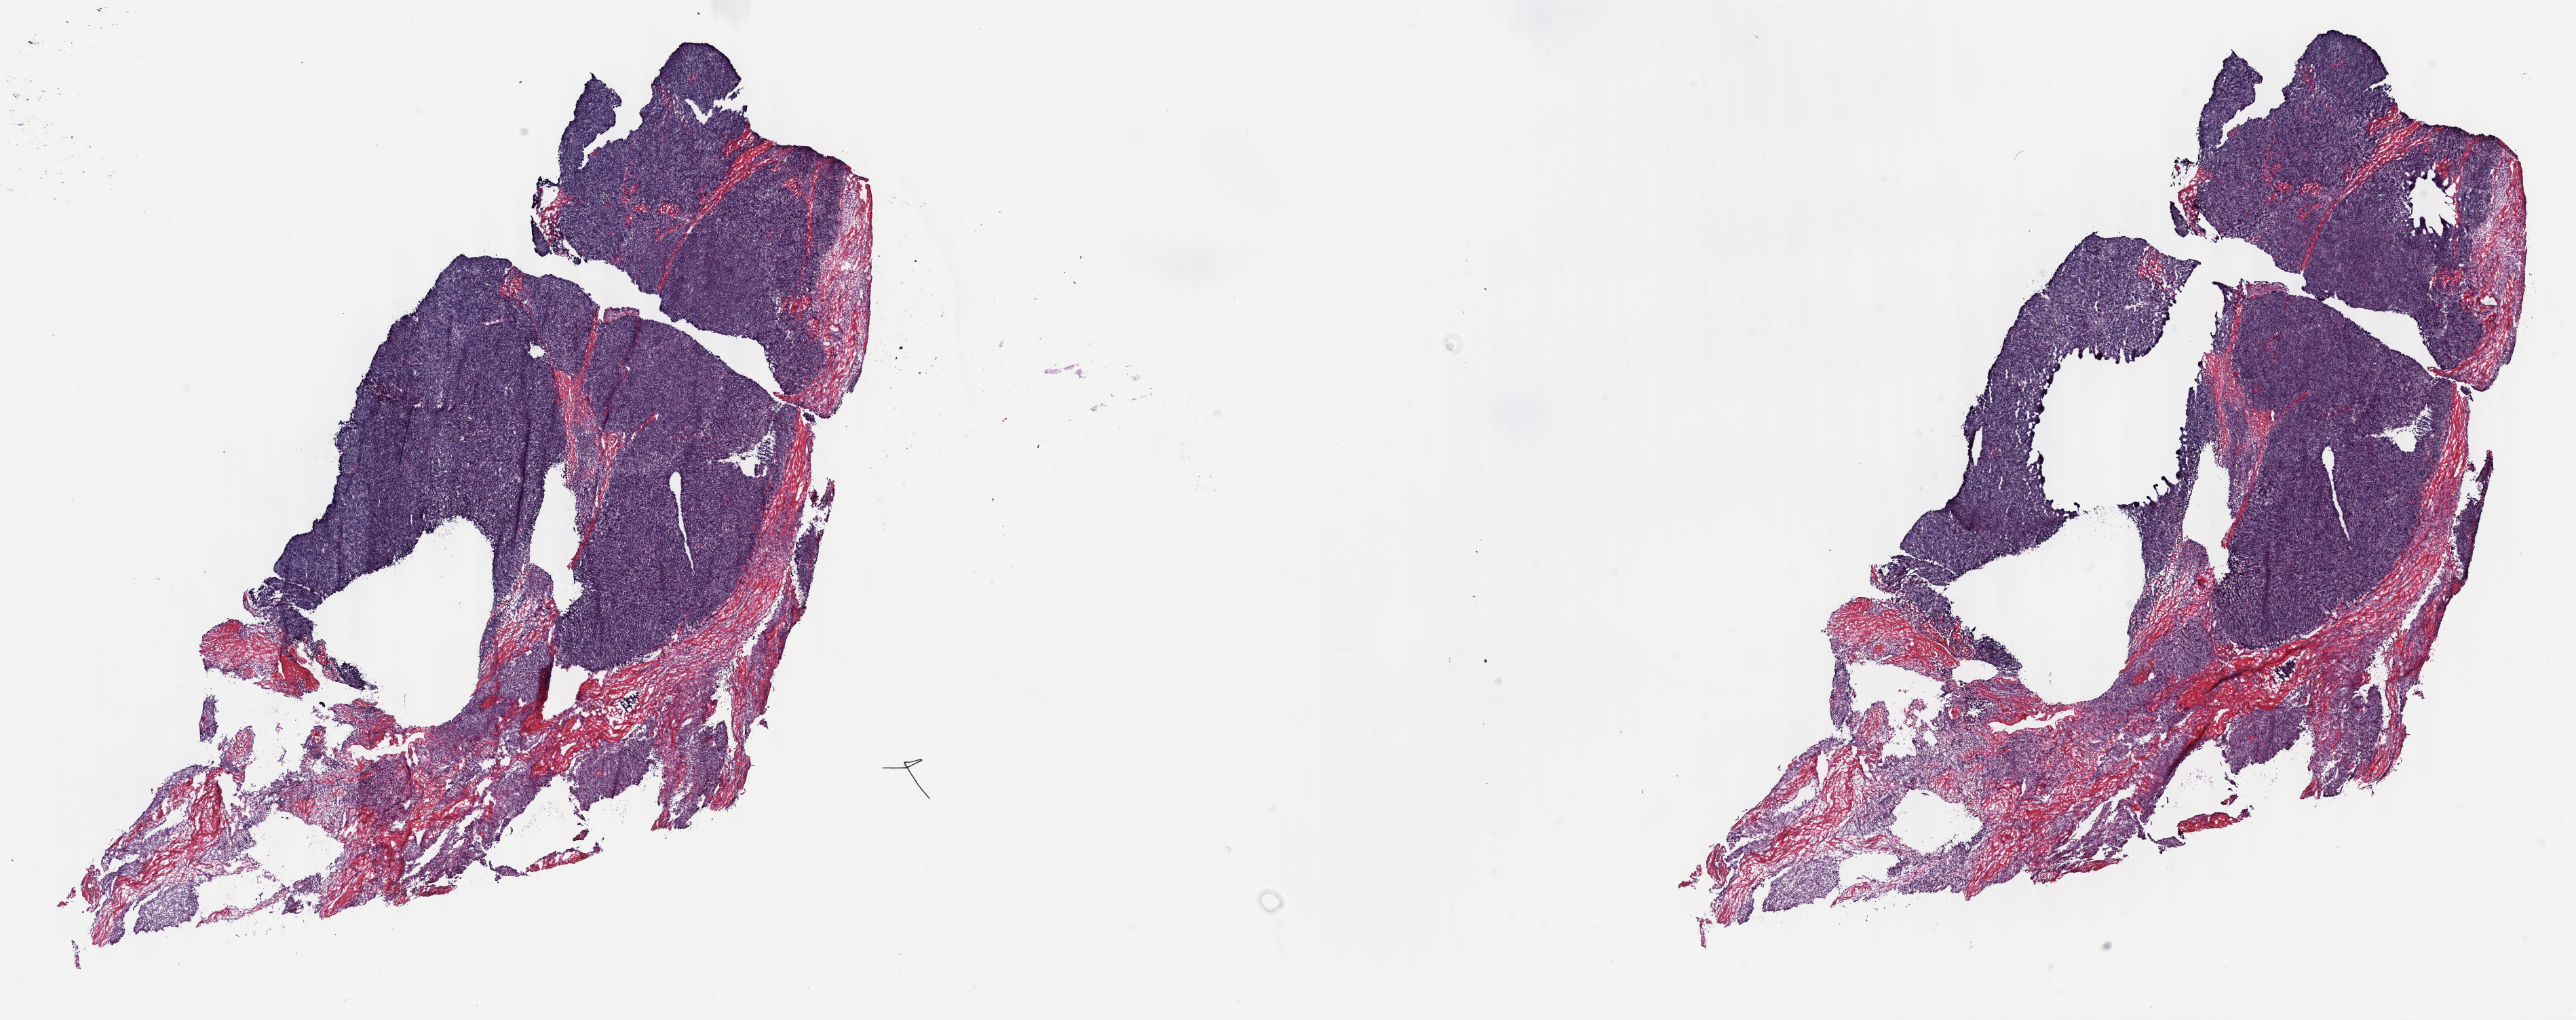
Digitized Hematoxylin and eosin (H&E) stained tissue section (whole slide), a low-resolution overview of the entire scanned area, about 30.7 x 12.2 mm; frozen section; sample: primary tumour, thymus. Patient: male, age at initial diagnosis 69 years. Pathologist review of this section (percent, as recorded): tumour cells 100%, tumour nuclei 65%, normal cells 0%, stromal cells 0%, necrosis 0%. Infiltration values recorded for this section: lymphocyte infiltration 5%, monocyte infiltration 0%, neutrophil infiltration 0%.
Pathologic diagnosis: Thymoma, type AB, malignant.